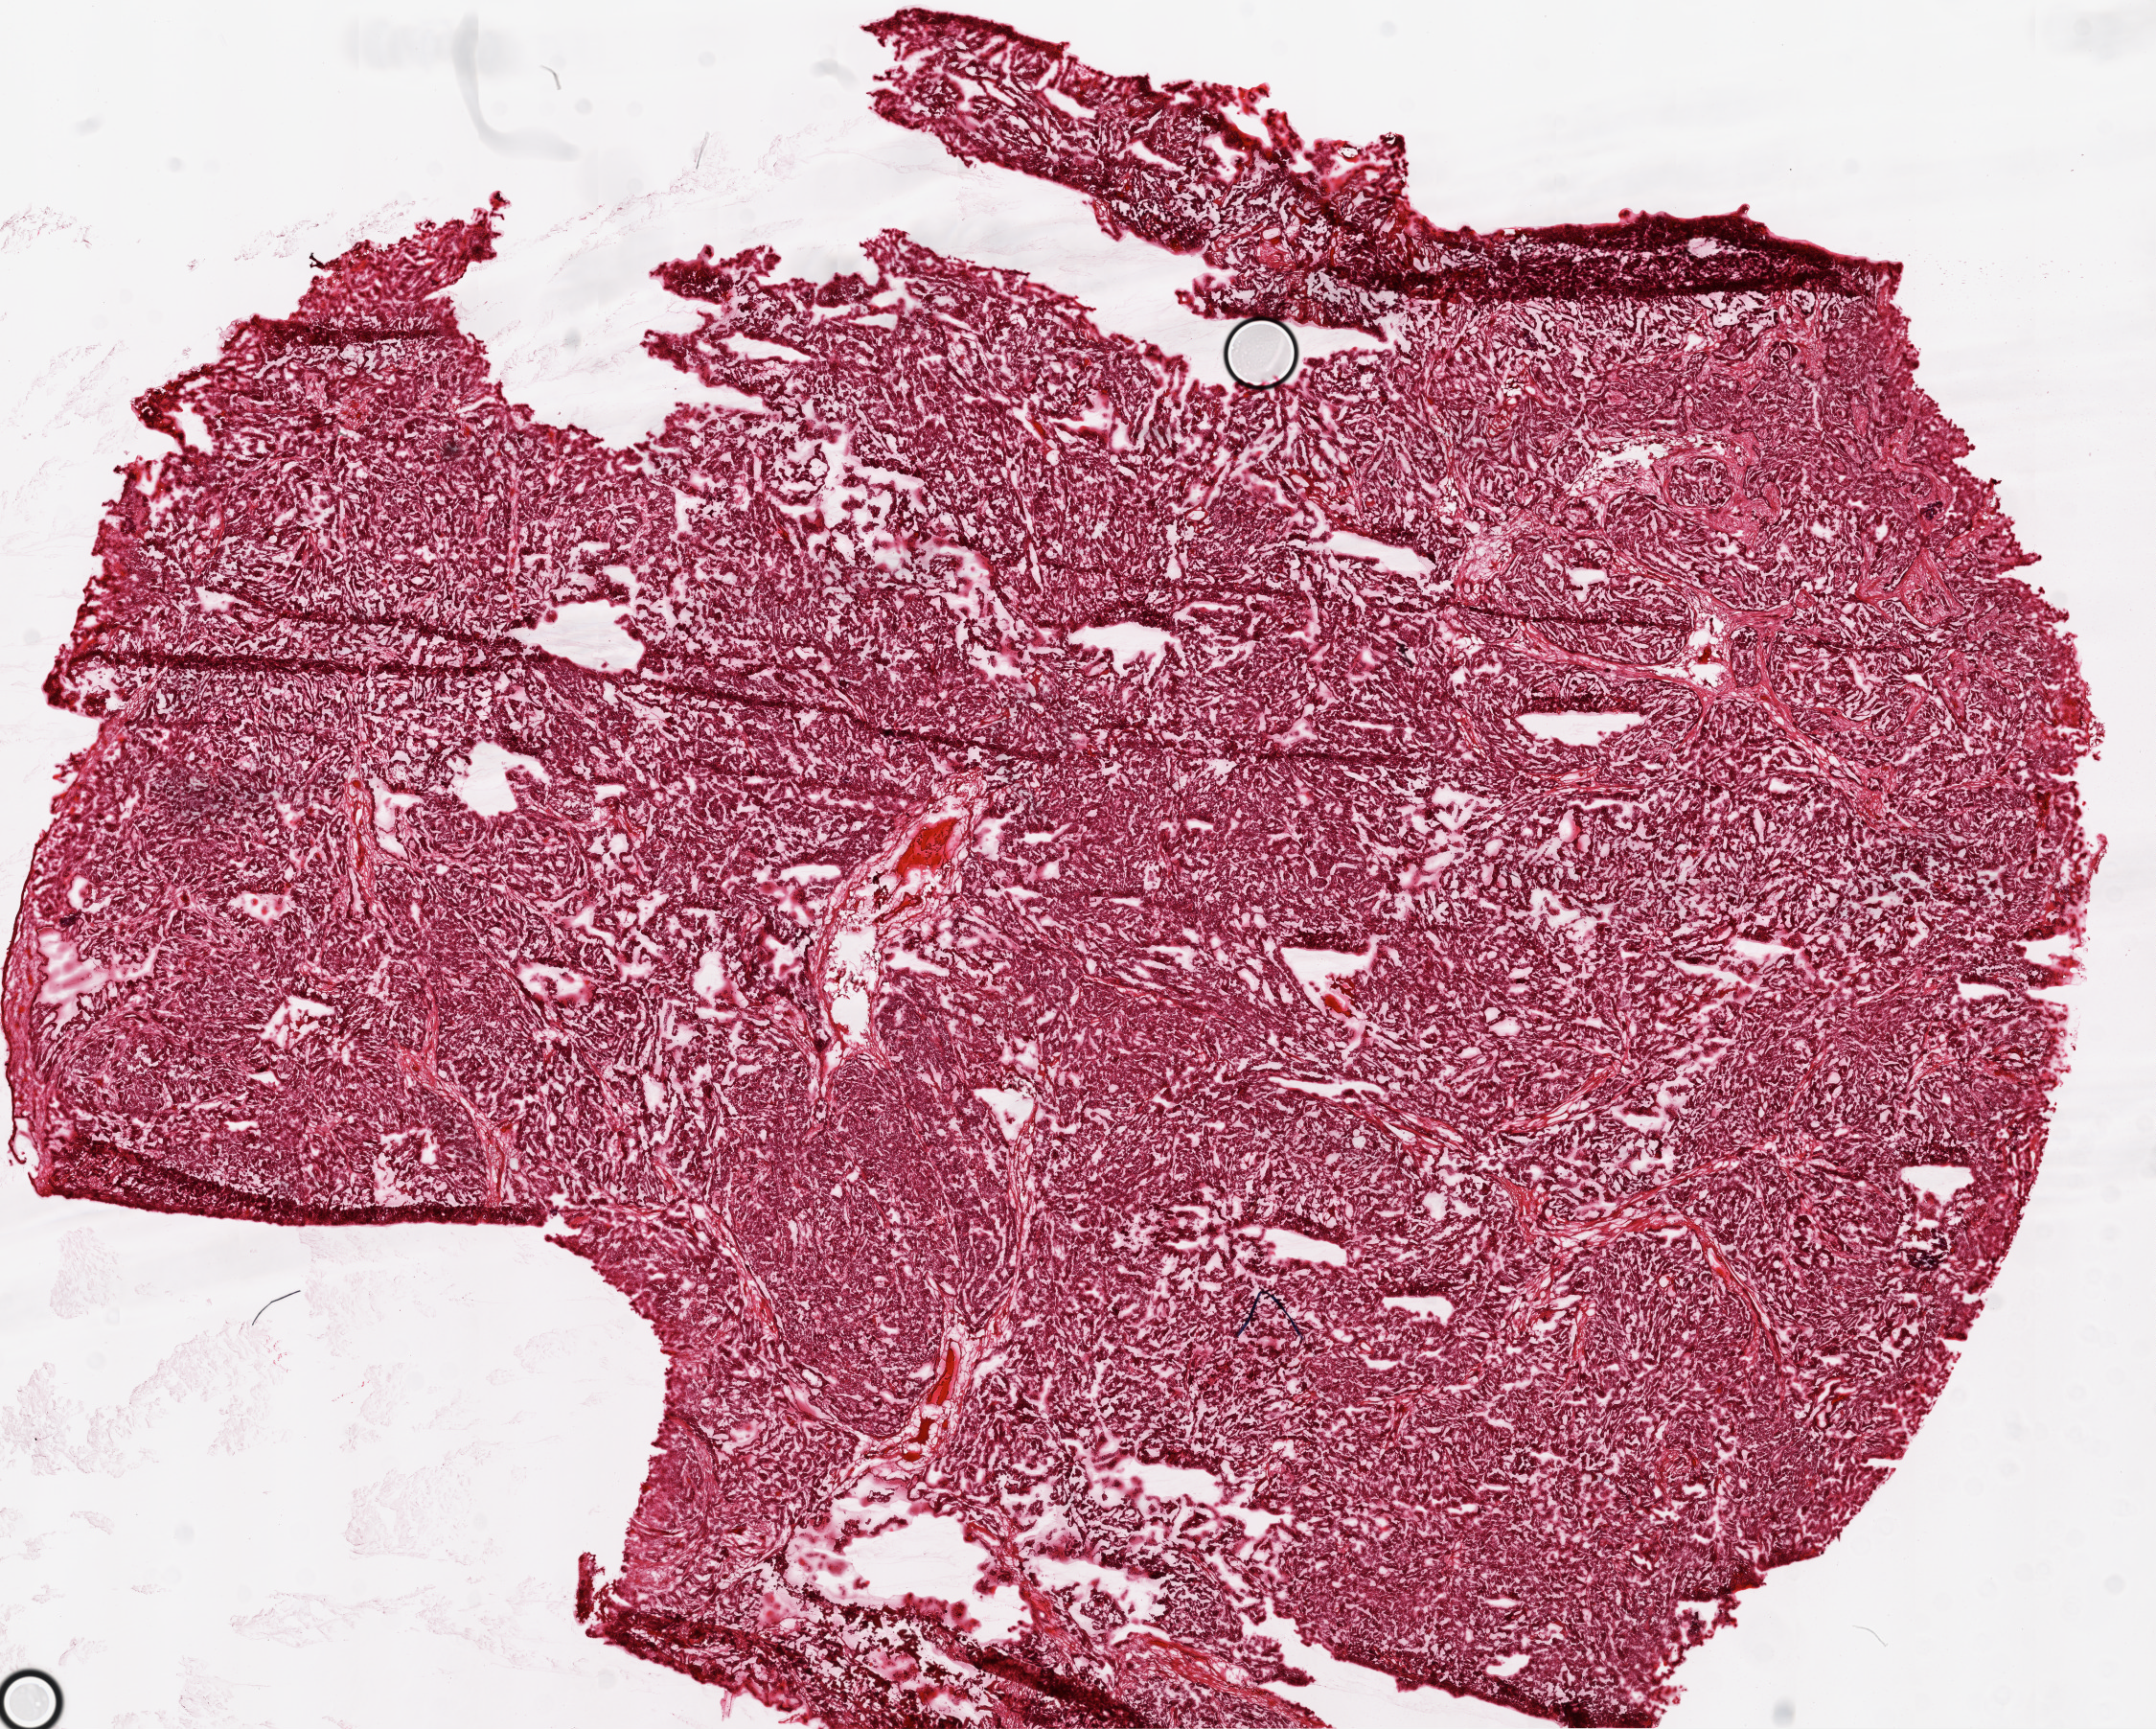
Digitized H&E tissue section (whole slide), low-resolution overview of the scanned area, about 18.1 x 14.5 mm, frozen section, primary tumour sample from the ovary. Patient: female, age at initial diagnosis 68 years. Histologic grade: G3 (poorly differentiated). Pathologist review of this section (percent, as recorded): tumour cells 95%, tumour nuclei 95%, normal cells 0%, stromal cells 5%, necrosis 0%.
- FIGO stage: IIIC
- pathologic diagnosis: Serous cystadenocarcinoma, NOS